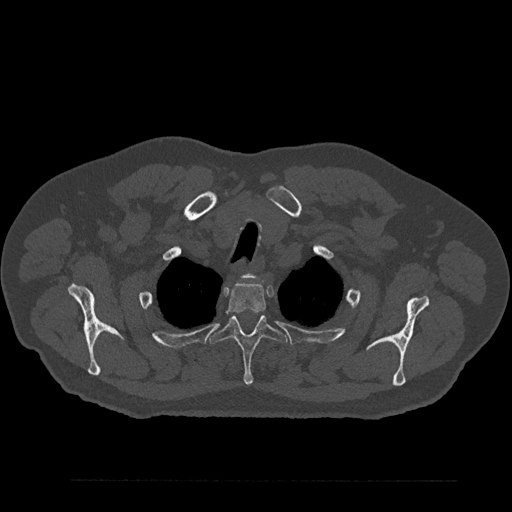
CT including the spine, one axial slice. Position 698 of 797 along the scan axis. Bone window (W 1800 / L 400 HU). 0.5 mm slice thickness. 512 × 512 image matrix. Patient: male, 61 years. From the clinical record (not read from this slice): primary cancer: prostate.
Annotated regions visible in this slice (semi-automatically segmented with operator editing):
- T1 vertebra: bounding box (x1, y1, x2, y2) in pixels: (248, 275, 252, 277)
- T2 vertebra: (226, 282, 266, 314)
- T3 vertebra: (211, 315, 287, 386)